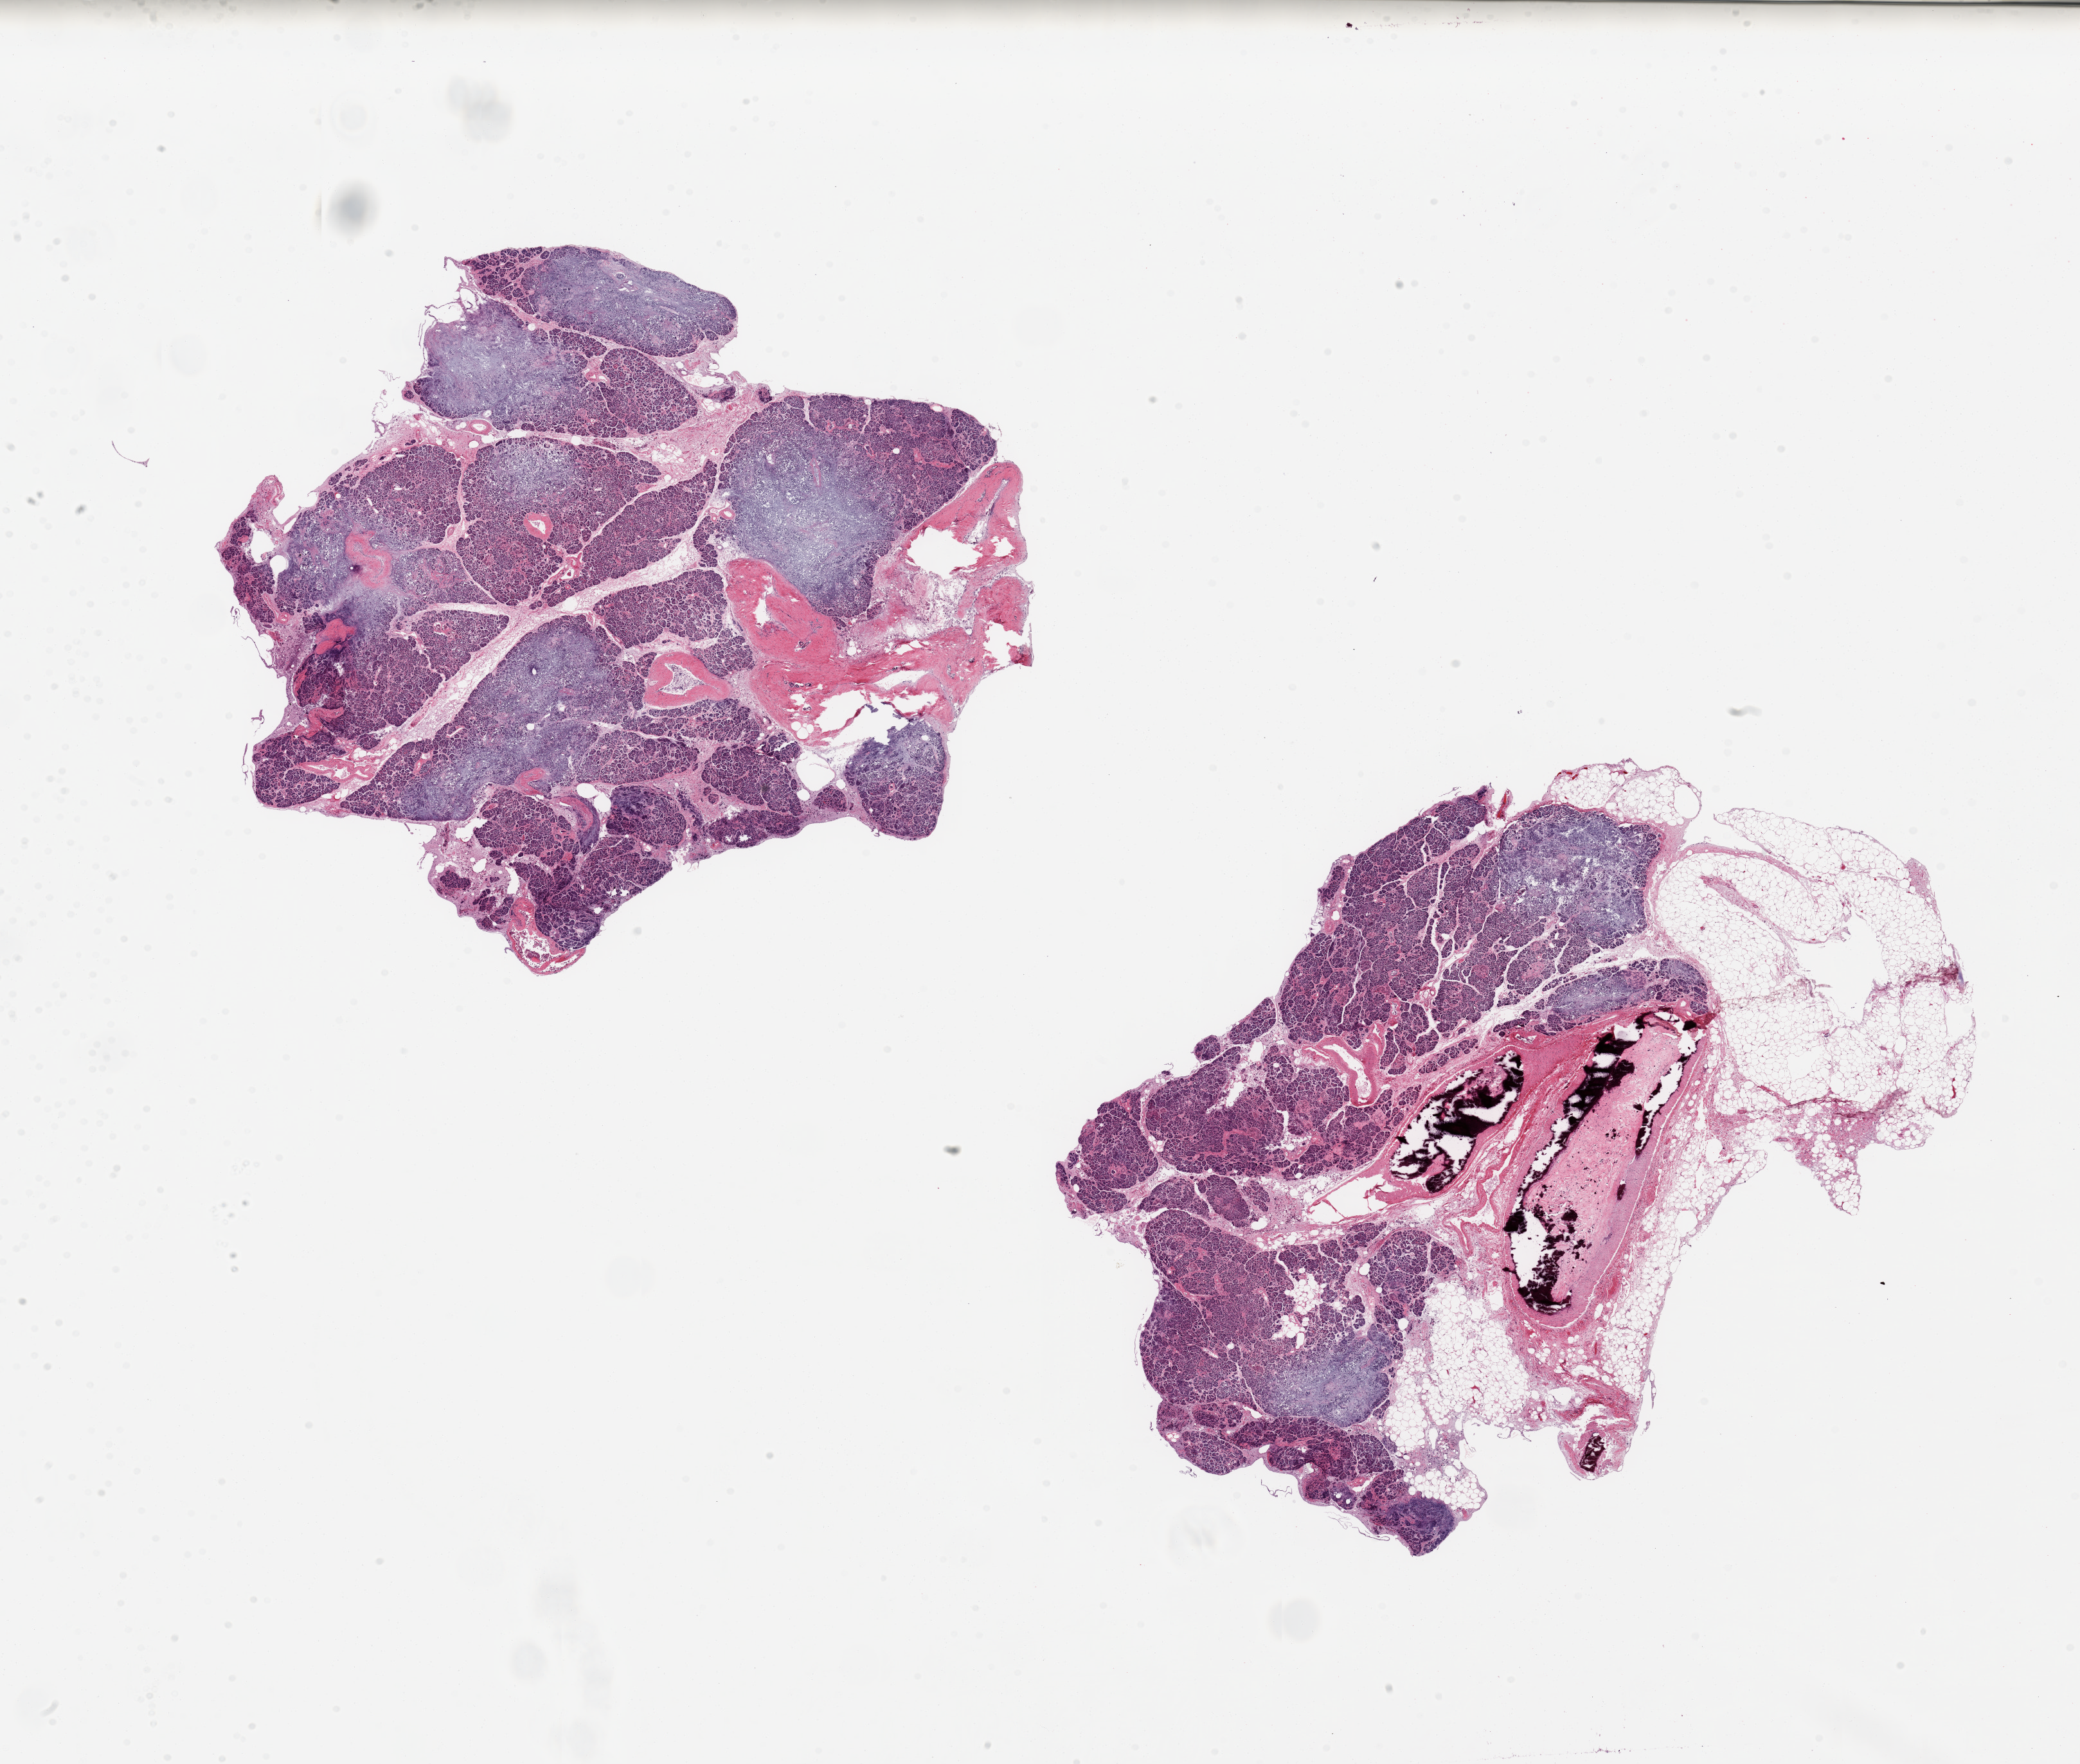
Digitized hematoxylin and eosin (H&E)-stained section — low-resolution overview of the scanned area, about 25.6 x 21.7 mm, PAXgene-fixed paraffin-embedded (PFPE) section, target tissue: pancreas, donor tissue sample. Female donor.
- review note (as recorded): 2 ~ 9x8.5mm aliquots, diffuse saponification, focally calcified